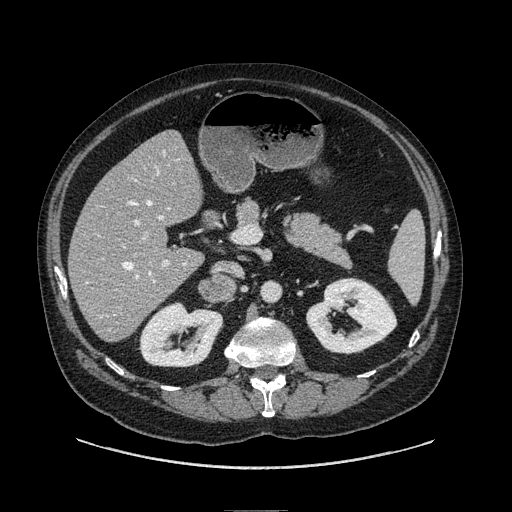
Contrast-enhanced abdominal CT, one axial slice; position 35 of 149 along the scan axis; soft-tissue window (W 400 / L 40 HU); 1.25 mm slice thickness; 512 × 512 image matrix. Male patient. Case-level facts recorded for this patient, not image findings: diagnosis: adrenocortical carcinoma; tumour side: right adrenal; tumour size at pathology: 7.5 cm; Ki-67 index: 15 %; stage (as recorded): 2.
Annotated regions visible in this slice (semi-automatically segmented with operator editing):
- mass: bounding box <201,275,232,303> (left, top, right, bottom; pixels)